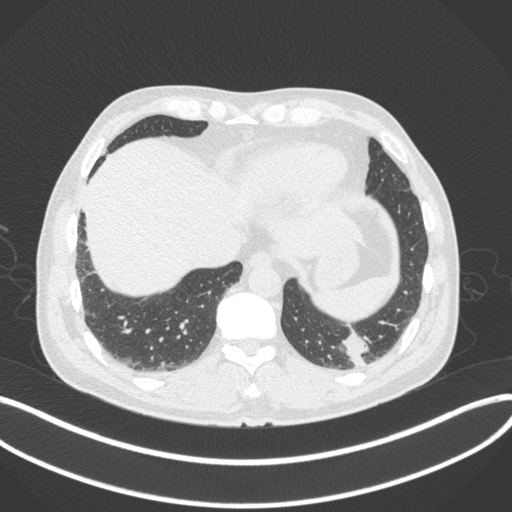
Chest CT, one axial slice; position 57 of 313 along the scan axis; reconstruction kernel B31f; 120 kVp; lung window (W 1500 / L -600 HU); 1 mm slice thickness; 512 × 512 image matrix, field of view 400 × 400 mm. Patient: male, 54 years. Case-level facts recorded for this patient, not image findings: clinical TNM (as recorded): T1c N0 M1; histopathological grade: G3.
Outlined on this slice (bounding box drawn by a radiologist):
- lung tumour (recorded histology: adenocarcinoma): bounding box [x1, y1, x2, y2] px = [337, 328, 369, 368]